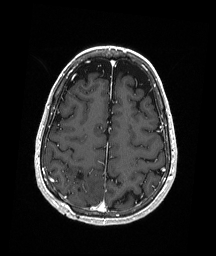
Brain MRI from a brain-tumour surgery series, one axial slice. Position 66 of 192 along the scan axis. T1-weighted post-contrast. 1 mm slice thickness. 216 × 256 image matrix. From the clinical record (not read from this slice): histopathology: Astrocytoma; WHO grade: 3; IDH mutation: yes.
Structures marked on this image (outlined manually by an expert reader):
- previous resection cavity: bounding box <76,172,84,191> (left, top, right, bottom; pixels)